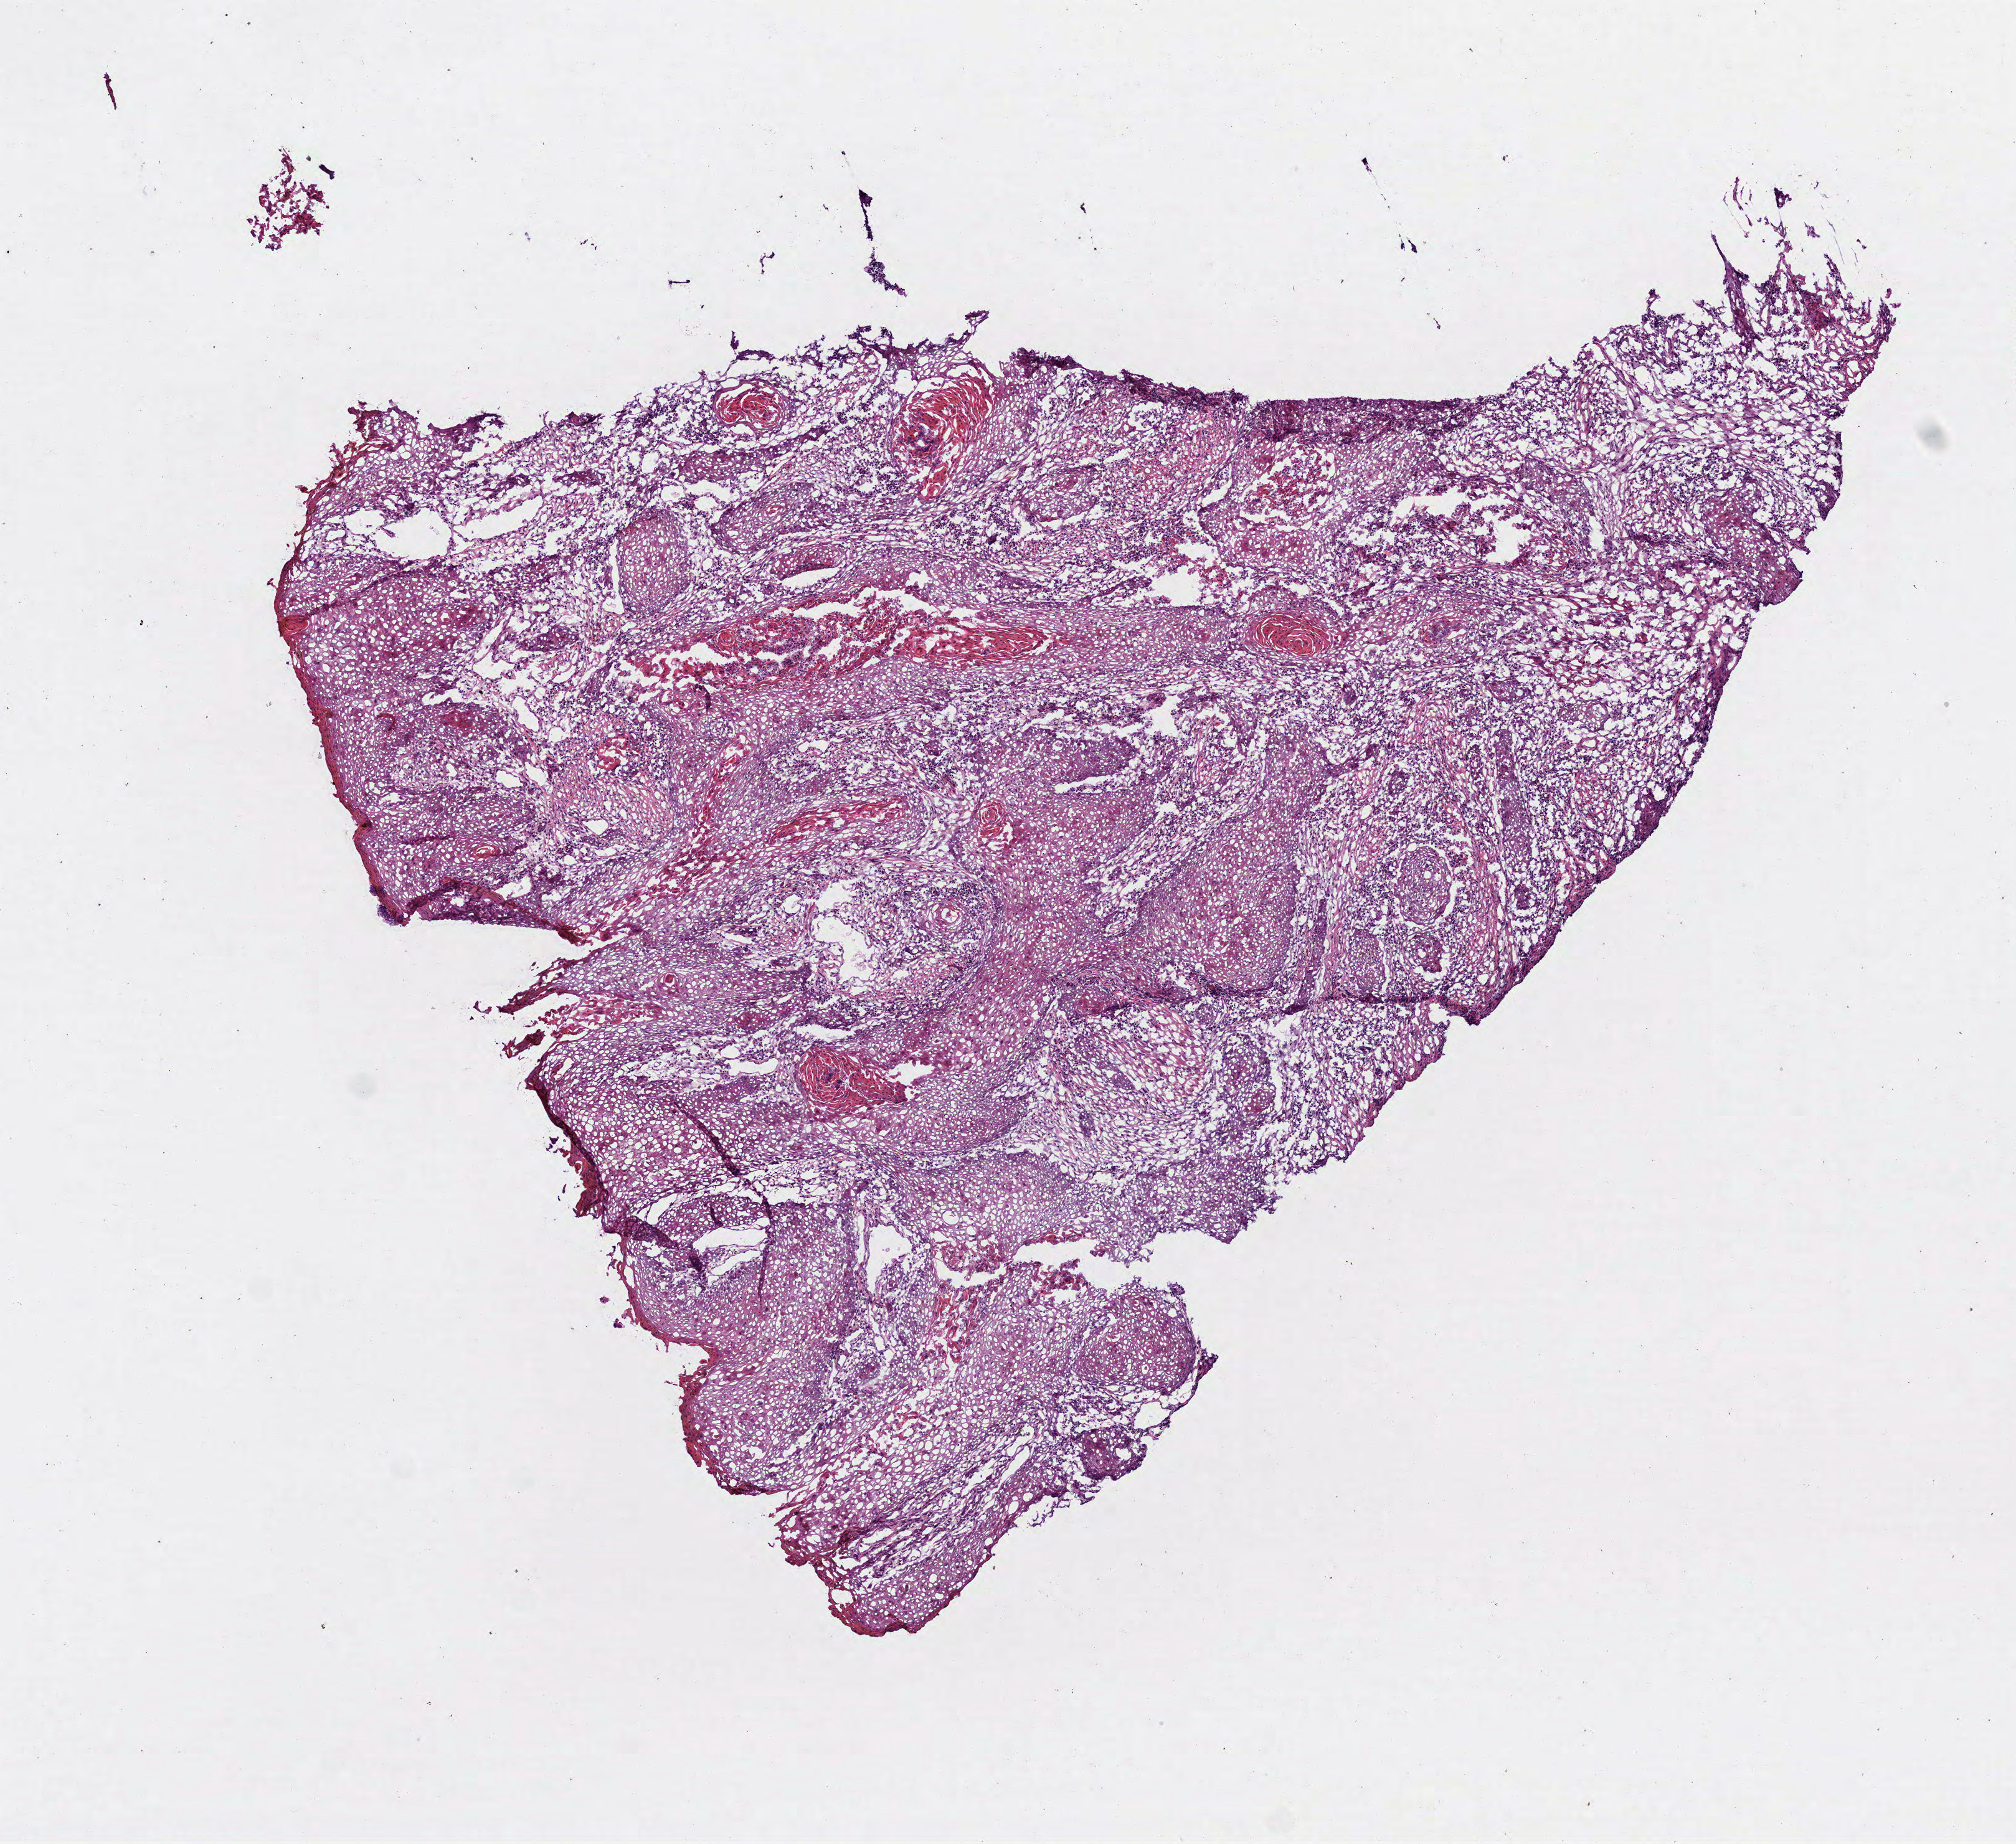
H&E-stained whole-slide image — a low-resolution overview of the entire scanned area, about 6.5 x 6.0 mm (from a 40x scan), frozen section from the bottom of the tissue portion, primary tumour sample from the head and neck. Male, age 63 years at initial diagnosis. Histologic grade: G2 (moderately differentiated). Slide review estimates, as recorded: tumour cells 85%, tumour nuclei 85%, normal cells 0%, stromal cells 15%, necrosis 0%.
AJCC pathologic stage: IVA (6th edition). Diagnosis: Squamous cell carcinoma, NOS. Laterality: right.